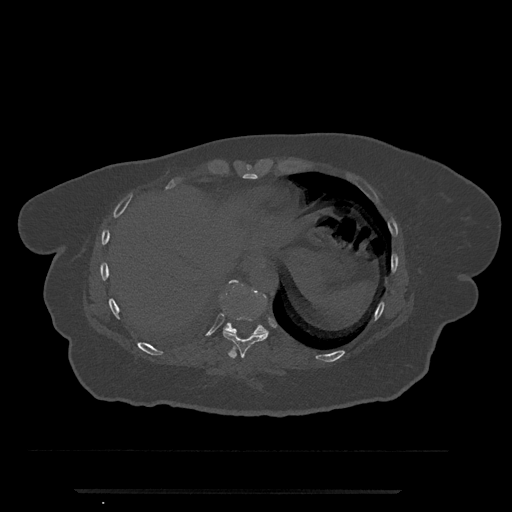
CT including the spine, one axial slice; slice 322 of 797 in the series (ordered by position); reconstruction kernel Br40s/3; bone window (W 1800 / L 400 HU); 0.5 mm slice thickness; 512 × 512 image matrix. Patient: female, 51 years. From the clinical record (not read from this slice): primary cancer: neuro; vertebrae with lytic lesions (as recorded): T8.
Outlined on this slice (semi-automatic segmentation, software-assisted and operator-edited):
- T10 vertebra: bounding box <223,280,267,336> (left, top, right, bottom; pixels)
- T9 vertebra: <223,316,269,358>